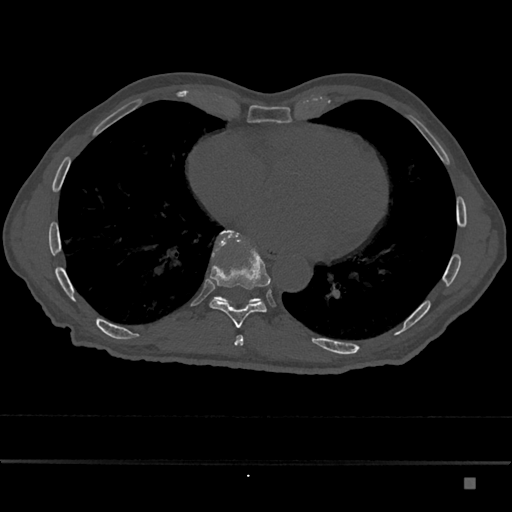
CT including the spine, one axial slice; position 791 of 797 along the scan axis; bone window (W 1800 / L 400 HU); 512 × 512 image matrix, field of view 390 × 390 mm. Male patient, age 72 years. From the clinical record (not read from this slice): primary cancer: prostate.
Outlined on this slice (semi-automatically segmented with operator editing):
- T10 vertebra: box from (x=213, y=231) to (x=263, y=304) px
- T9 vertebra: (x=209, y=230)–(x=271, y=328)